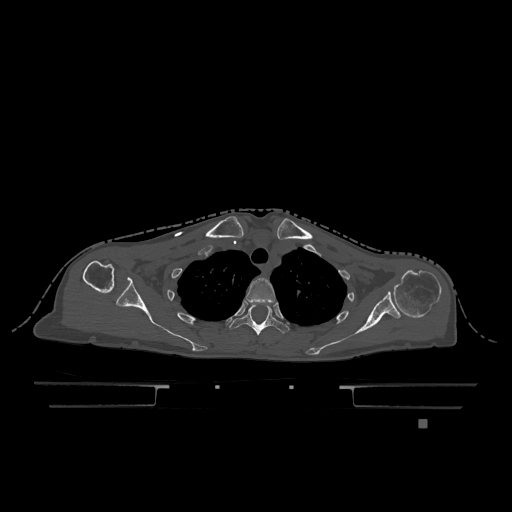
CT including the spine, one axial slice. Slice 937 of 1317 in the series (ordered by position). Bone window (W 1800 / L 400 HU). 0.5 mm slice thickness. 512 × 512 image matrix, field of view 500 × 500 mm. Patient: female, 74 years. From the clinical record (not read from this slice): primary cancer: lung.
Outlined on this slice (semi-automatic segmentation, software-assisted and operator-edited):
- T2 vertebra: box from (x=246, y=278) to (x=276, y=305) px
- T3 vertebra: (x=230, y=305)–(x=289, y=336)